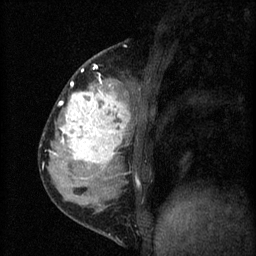
Breast MRI (dynamic contrast-enhanced), one sagittal slice. Slice 20 of 60 in the series (ordered by position). 3 images stored at this slice position (order not interpretable as contrast timing). 1.5 T. TE 4.2 ms, TR 8.2 ms. 256 × 256 image matrix, field of view 180 × 180 mm. Patient: female, 37 years.
Structures marked on this image (semi-automatic segmentation, software-assisted and operator-edited):
- analysis volume of interest (the breast-tissue region the enhancement analysis was run in; not a lesion): bounding box (x1, y1, x2, y2) in pixels: (53, 78, 140, 181)
- tumour enhancement mask (voxels above the 70 % enhancement threshold inside the analysis volume of interest): (54, 80, 130, 169)